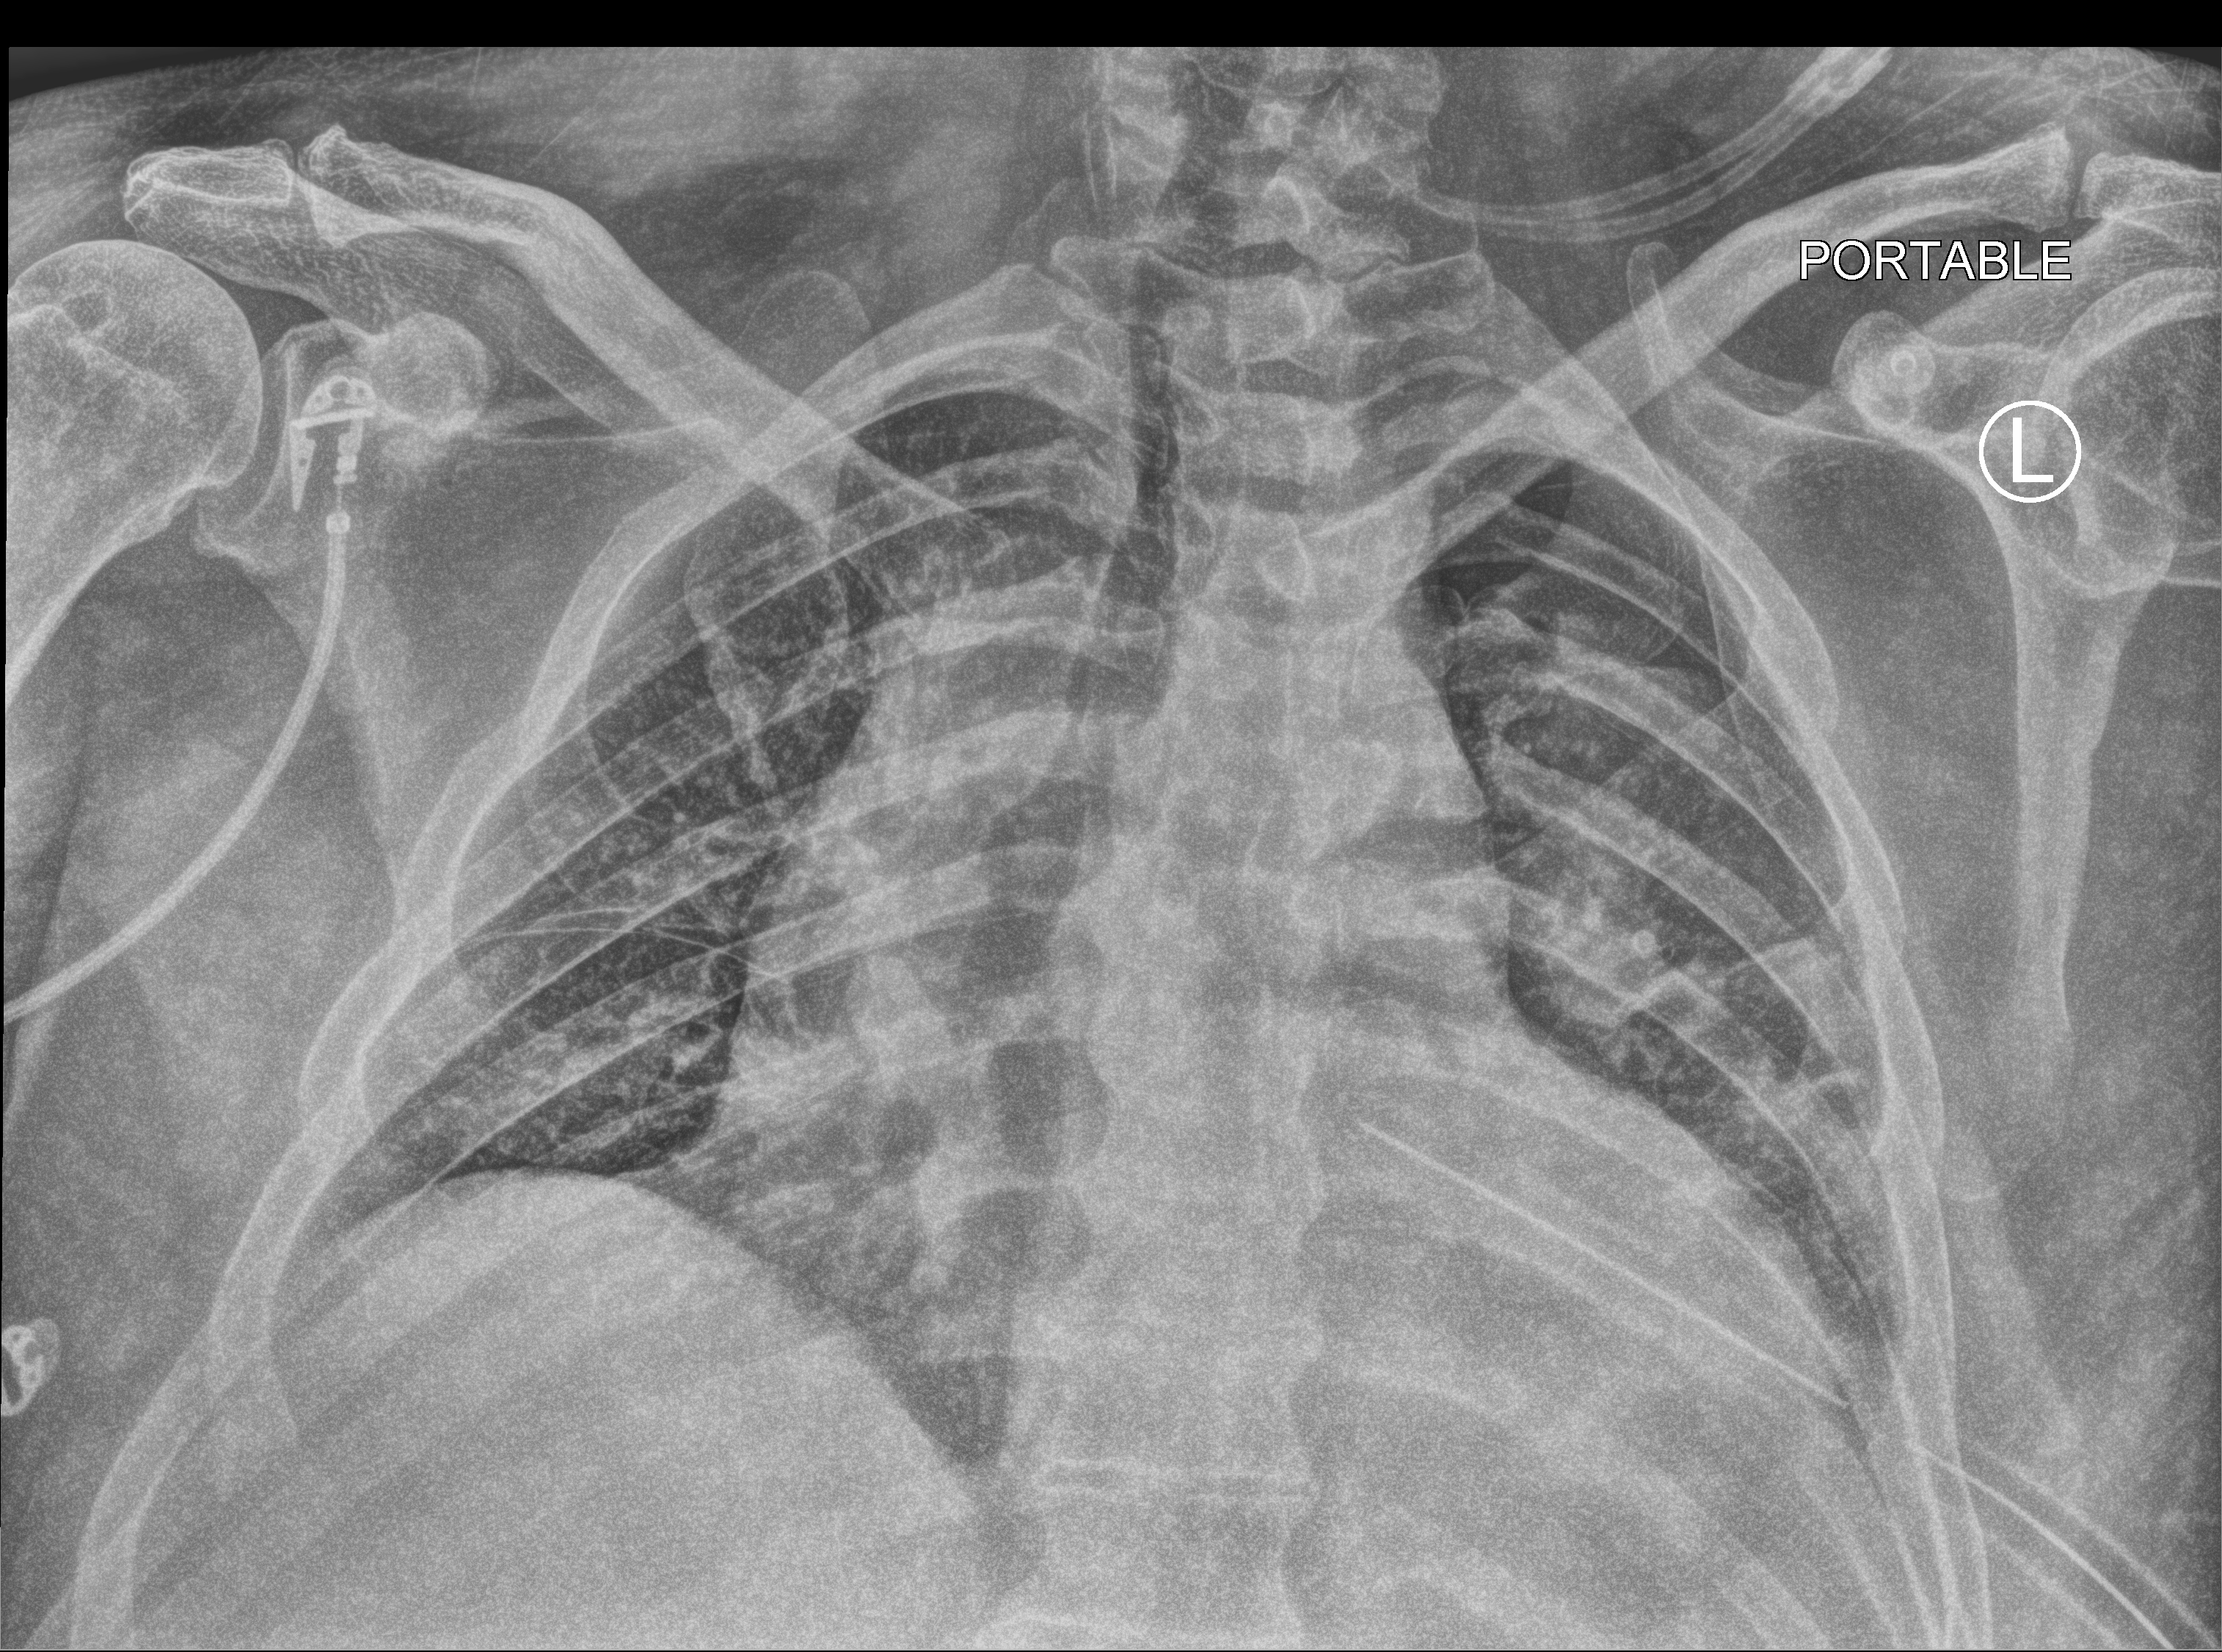
Bedside chest radiograph (computed radiography), anteroposterior (AP) projection. Male patient hospitalised with COVID-19, age 18–59 years.
Admission-level facts for this patient (not findings on this image; timing relative to this image not recorded): length of hospital stay: 10 days; admitted to intensive care during this hospital stay: no.